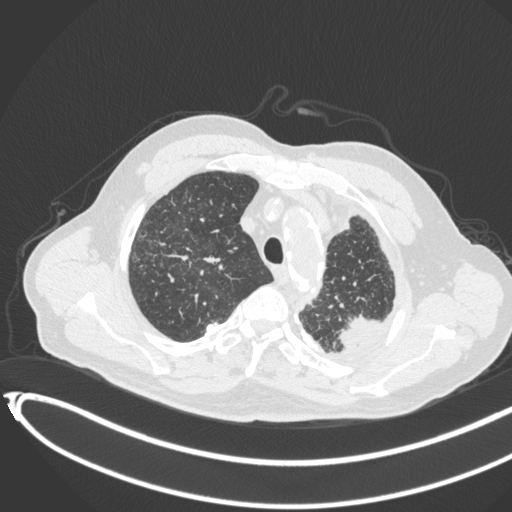
Chest CT, one axial slice; position 347 of 451 along the scan axis; reconstruction kernel B31f; lung window (W 1500 / L -600 HU); 1 mm slice thickness; 512 × 512 image matrix, field of view 400 × 400 mm. Patient: male, 78 years. Case-level facts recorded for this patient, not image findings: clinical TNM (as recorded): T1c N0 M1.
Structures marked on this image (bounding box drawn by a radiologist):
- lung tumour (recorded histology: adenocarcinoma): bounding box (x1, y1, x2, y2) in pixels: (335, 310, 394, 354)